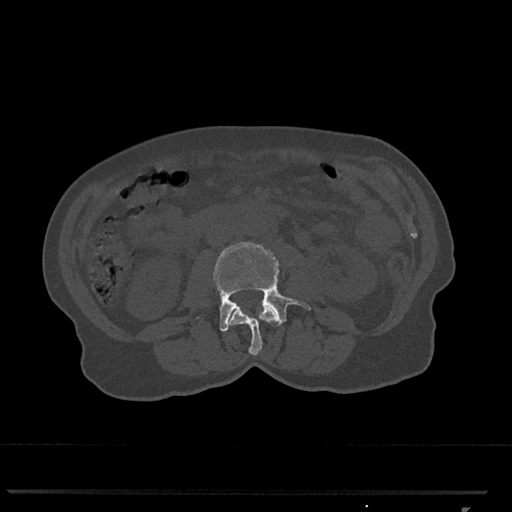
CT including the spine, one axial slice; reconstruction kernel Br40s/3; 120 kVp; bone window (W 1800 / L 400 HU); 0.5 mm slice thickness; 512 × 512 image matrix, field of view 380 × 380 mm. Female patient, age 62 years. Case-level facts recorded for this patient, not image findings: primary cancer: renal.
Annotated regions visible in this slice (semi-automatic segmentation, software-assisted and operator-edited):
- L2 vertebra: bounding box [x1, y1, x2, y2] px = [228, 306, 278, 355]
- L3 vertebra: [214, 242, 311, 332]